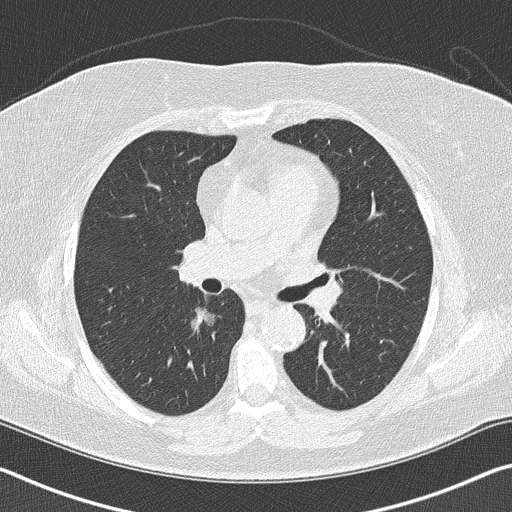
Axial slice from a low-dose chest CT screening exam; baseline annual screen; lung window (W 1500 / L -600 HU); 2 mm slice thickness; lung (sharp) reconstruction kernel (B50f). Female participant, aged 60 years at enrolment.
Expert reader's lesion annotation, box from (x=173, y=294) to (x=228, y=344) px. The screening reader recorded 2 non-calcified nodules or masses ≥4 mm on this exam (right lower lobe, left upper lobe); which of them this box marks is not recorded. Official screen result: positive, change unspecified: nodule(s) >= 4 mm or enlarging nodule(s), mass(es), or other non-specific abnormalities suspicious for lung cancer. Later outcome: lung cancer diagnosed 482 days after this screen — bronchiolo-alveolar carcinoma, non-mucinous, right lower lobe, stage IA (AJCC 6th edition), 15 mm at pathology.